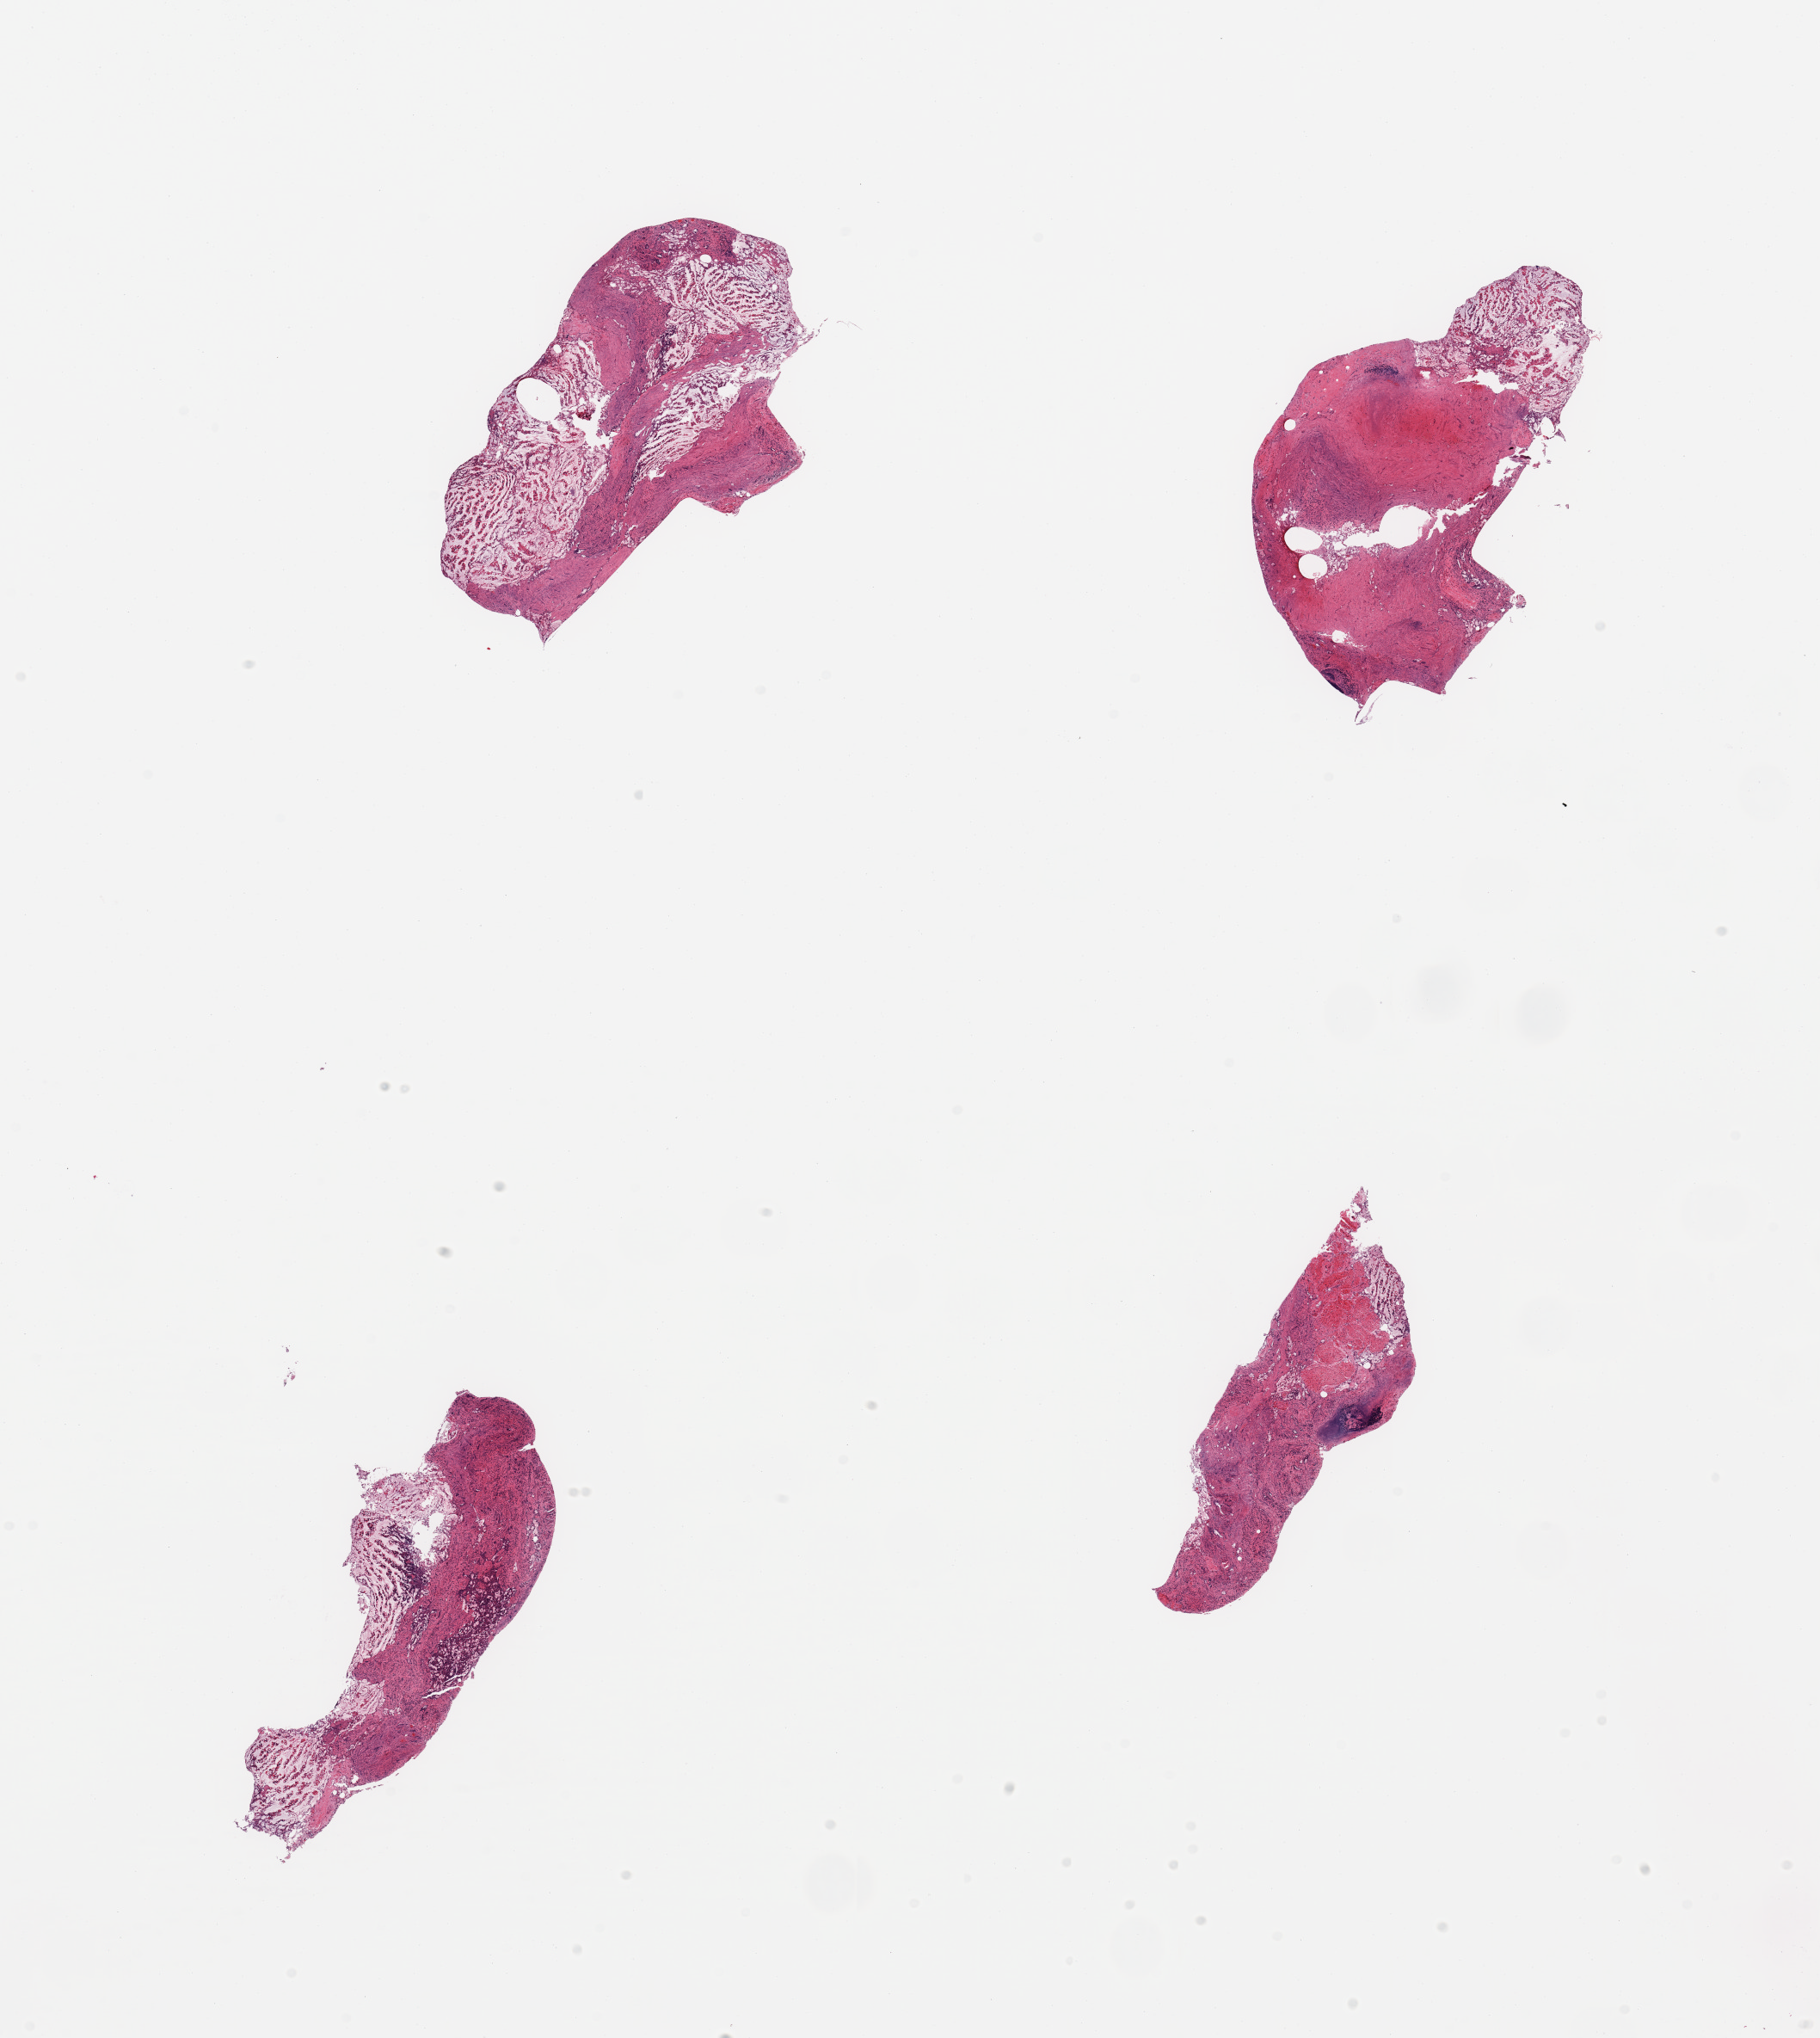
H&E whole-slide image — whole scanned area (about 16.7 x 18.7 mm) shown as a low-resolution overview; PAXgene-fixed paraffin-embedded (PFPE) section; sampled site (target tissue): ileum; donor tissue sample. Donor sex: male.
• reviewer comment on this tissue sample: 4 pieces; autolyzed mucosa with only focal lymphoid tissue and portion of muscularis (not target)